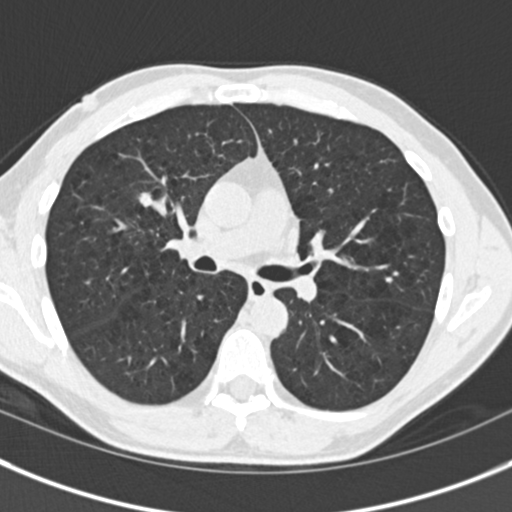
Low-dose screening chest CT, one axial slice. Position 100 of 175 along the scan axis. Reconstruction kernel B30f. Lung window (W 1500 / L -600 HU). 2 mm slice thickness. 512 × 512 image matrix, field of view 306 × 306 mm.
Structures marked on this image (expert manual segmentation):
- lesion 1 (tumor, upper lobe of right lung): bounding box (x1, y1, x2, y2) in pixels: (138, 192, 153, 207)